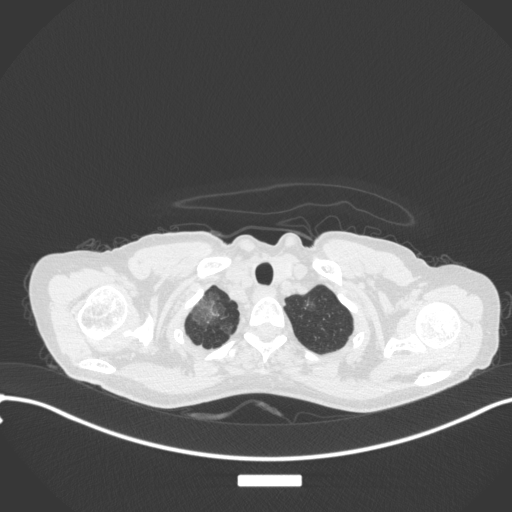
Chest CT, one axial slice; slice 308 of 311 in the series (ordered by position); reconstruction kernel B31f; 120 kVp; lung window (W 1500 / L -600 HU); 512 × 512 image matrix, field of view 400 × 400 mm. Female patient, age 59 years. Case-level facts recorded for this patient, not image findings: clinical TNM (as recorded): T3 N0 M0.
Outlined on this slice (bounding box drawn by a radiologist):
- lung tumour (recorded histology: adenocarcinoma): bounding box (x1, y1, x2, y2) in pixels: (189, 297, 220, 324)